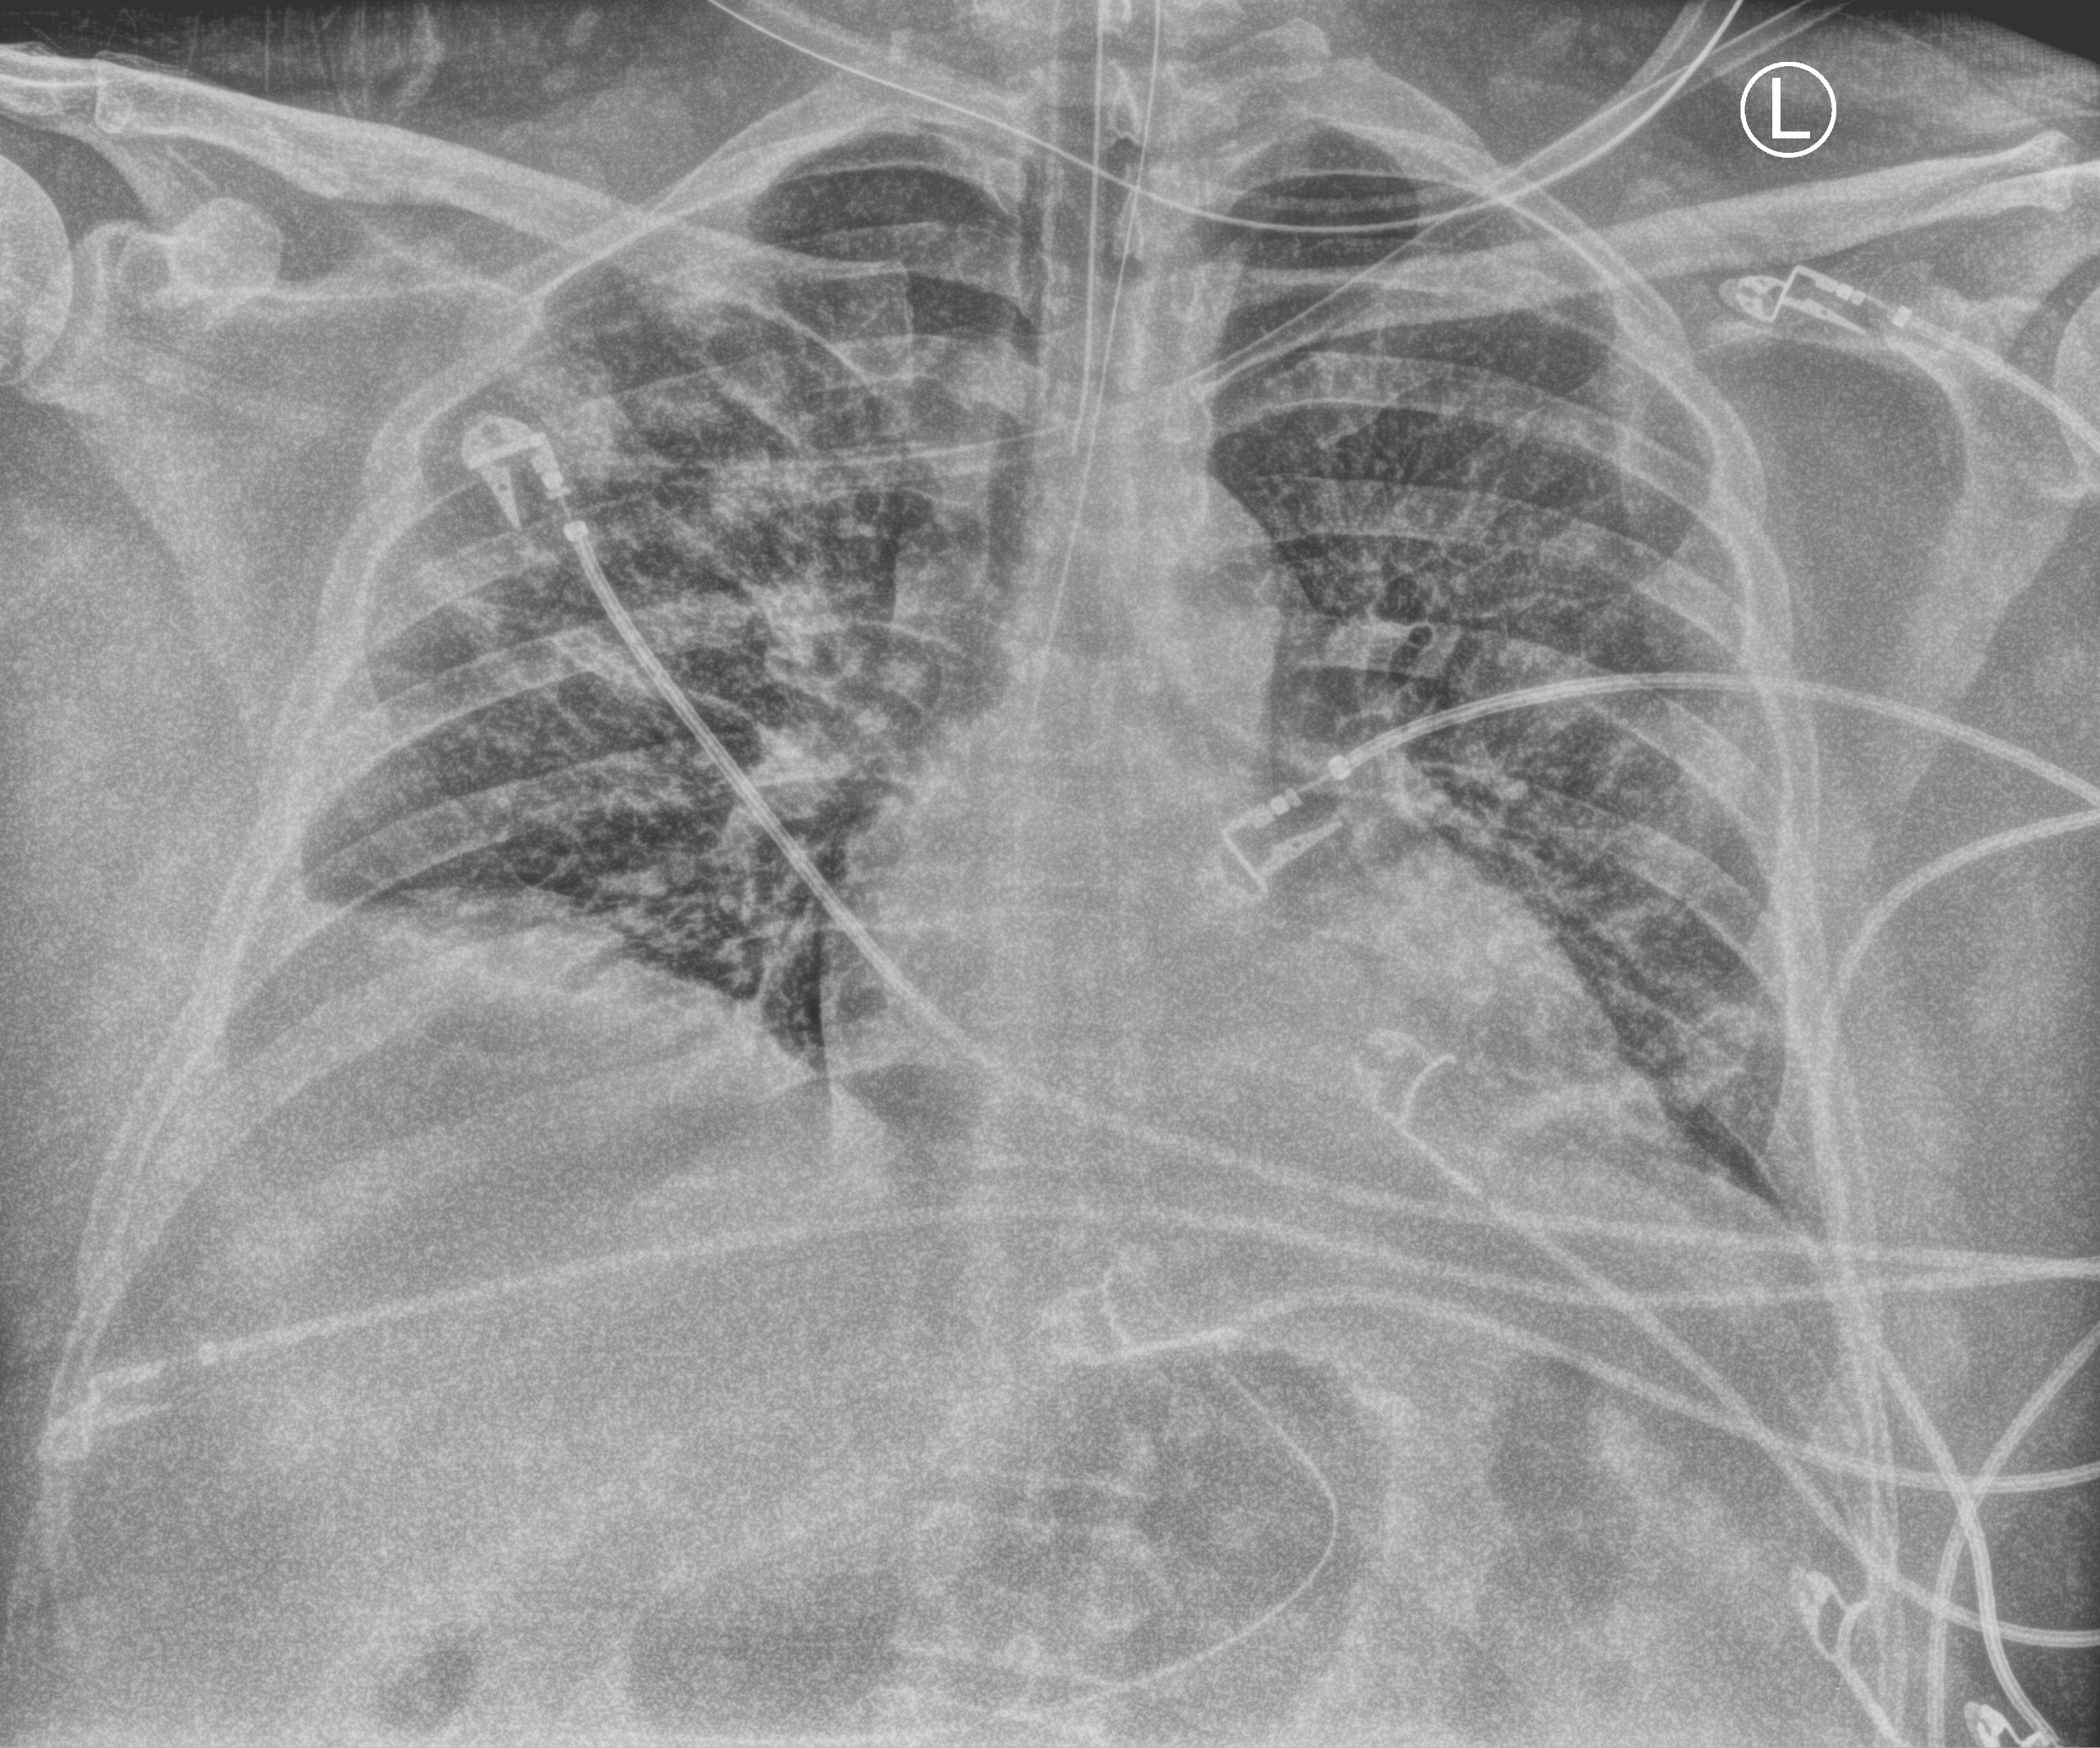
Chest X-ray (portable). Patient hospitalised with COVID-19, aged 18–59 years.
Hospital-stay facts (about this admission, not read from this image; timing relative to this image not recorded): admitted to intensive care during this hospital stay: yes; mechanically ventilated during this hospital stay: yes; length of hospital stay: 16 days.